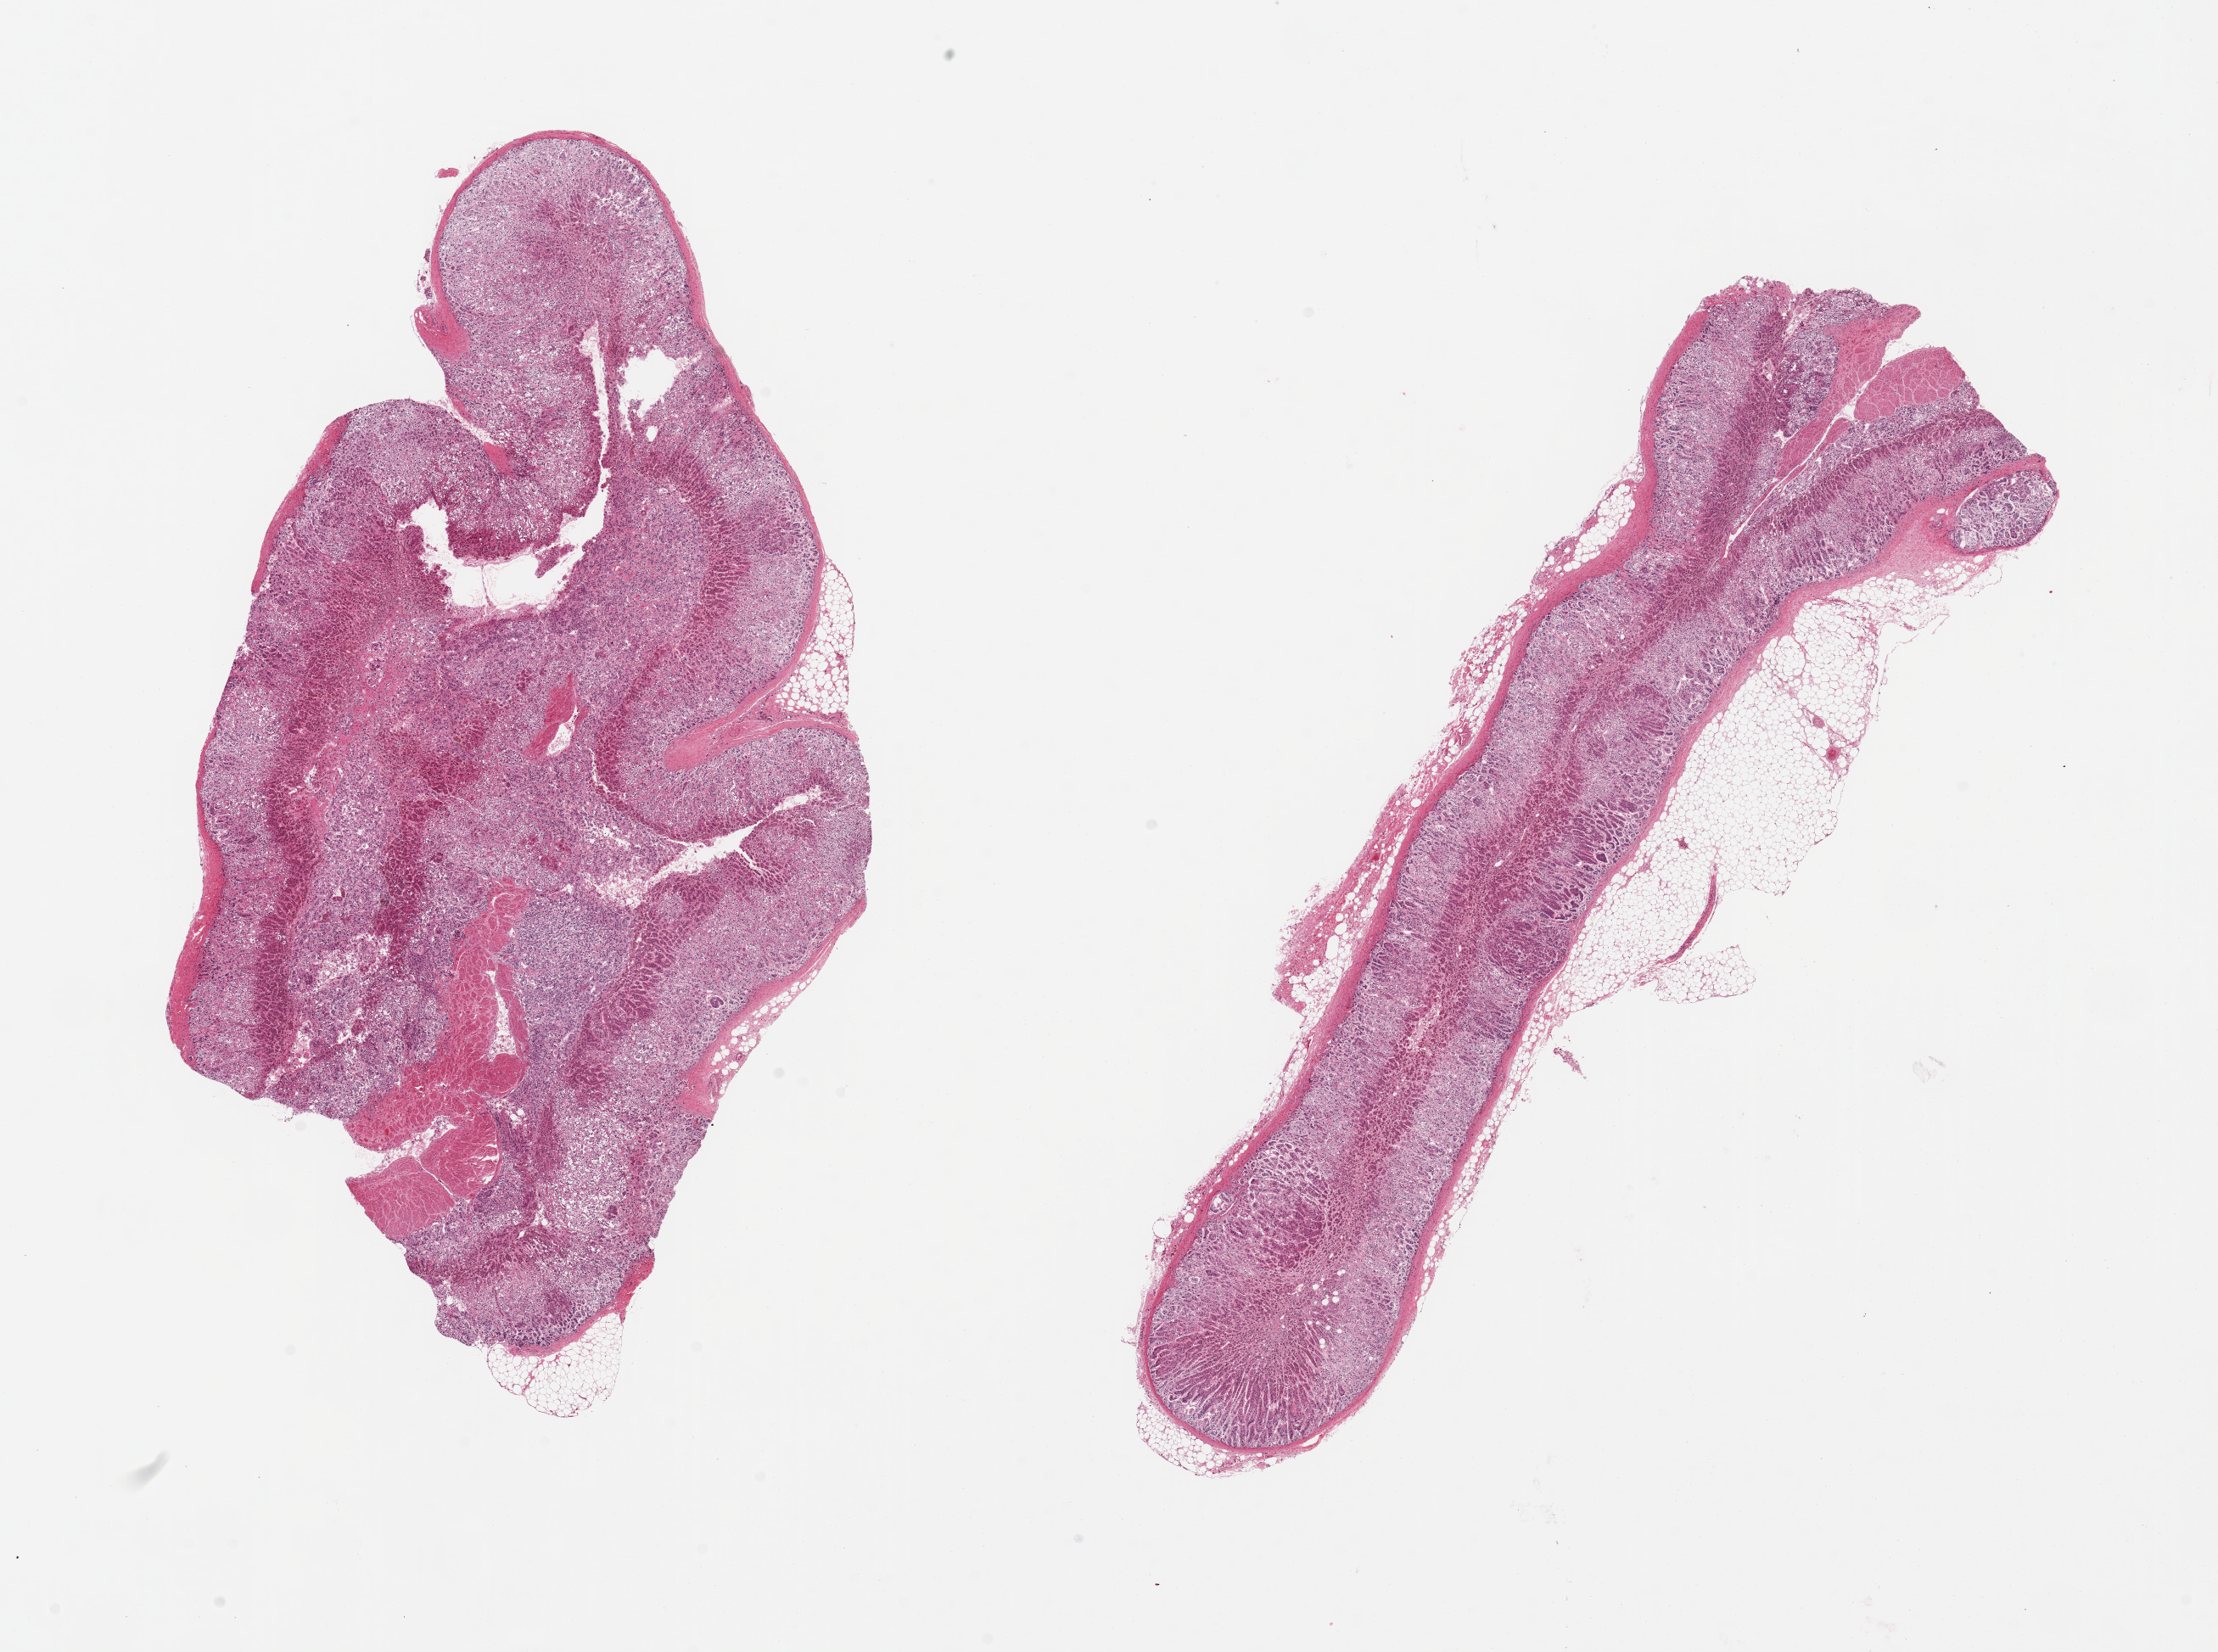
Haematoxylin and eosin whole-slide image, brightfield — shown as a low-resolution overview of the whole scanned area (about 20.7 x 15.4 mm, from a 20x scan), PAXgene-fixed, paraffin-embedded tissue, section of adrenal gland (target tissue), tissue donor sample. Donor: male.
Reviewer comment on this tissue sample: 2 pieces. 12x6 & 13x4mm; focal adherent fat ~1mm nubbin, all cortex, generally poorly preserved.